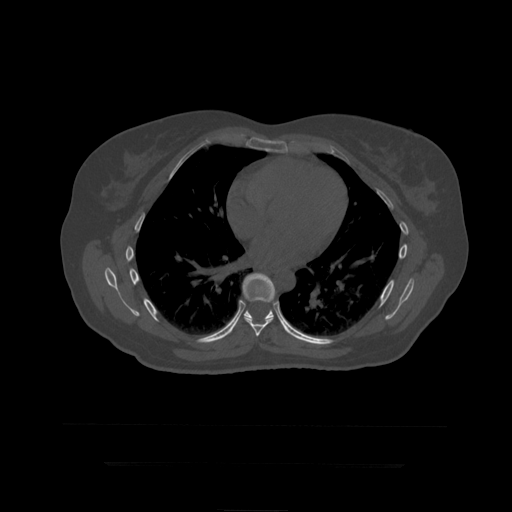
CT including the spine, one axial slice; slice 274 of 399 in the series (ordered by position); reconstruction kernel STANDARD; bone window (W 1800 / L 400 HU); 1.25 mm slice thickness; 512 × 512 image matrix, field of view 450 × 450 mm. Patient age 41 years. Case-level facts recorded for this patient, not image findings: primary cancer: breast.
Structures marked on this image (semi-automatic segmentation, software-assisted and operator-edited):
- T8 vertebra: bounding box <243,273,275,337> (left, top, right, bottom; pixels)
- T9 vertebra: <229,275,293,336>